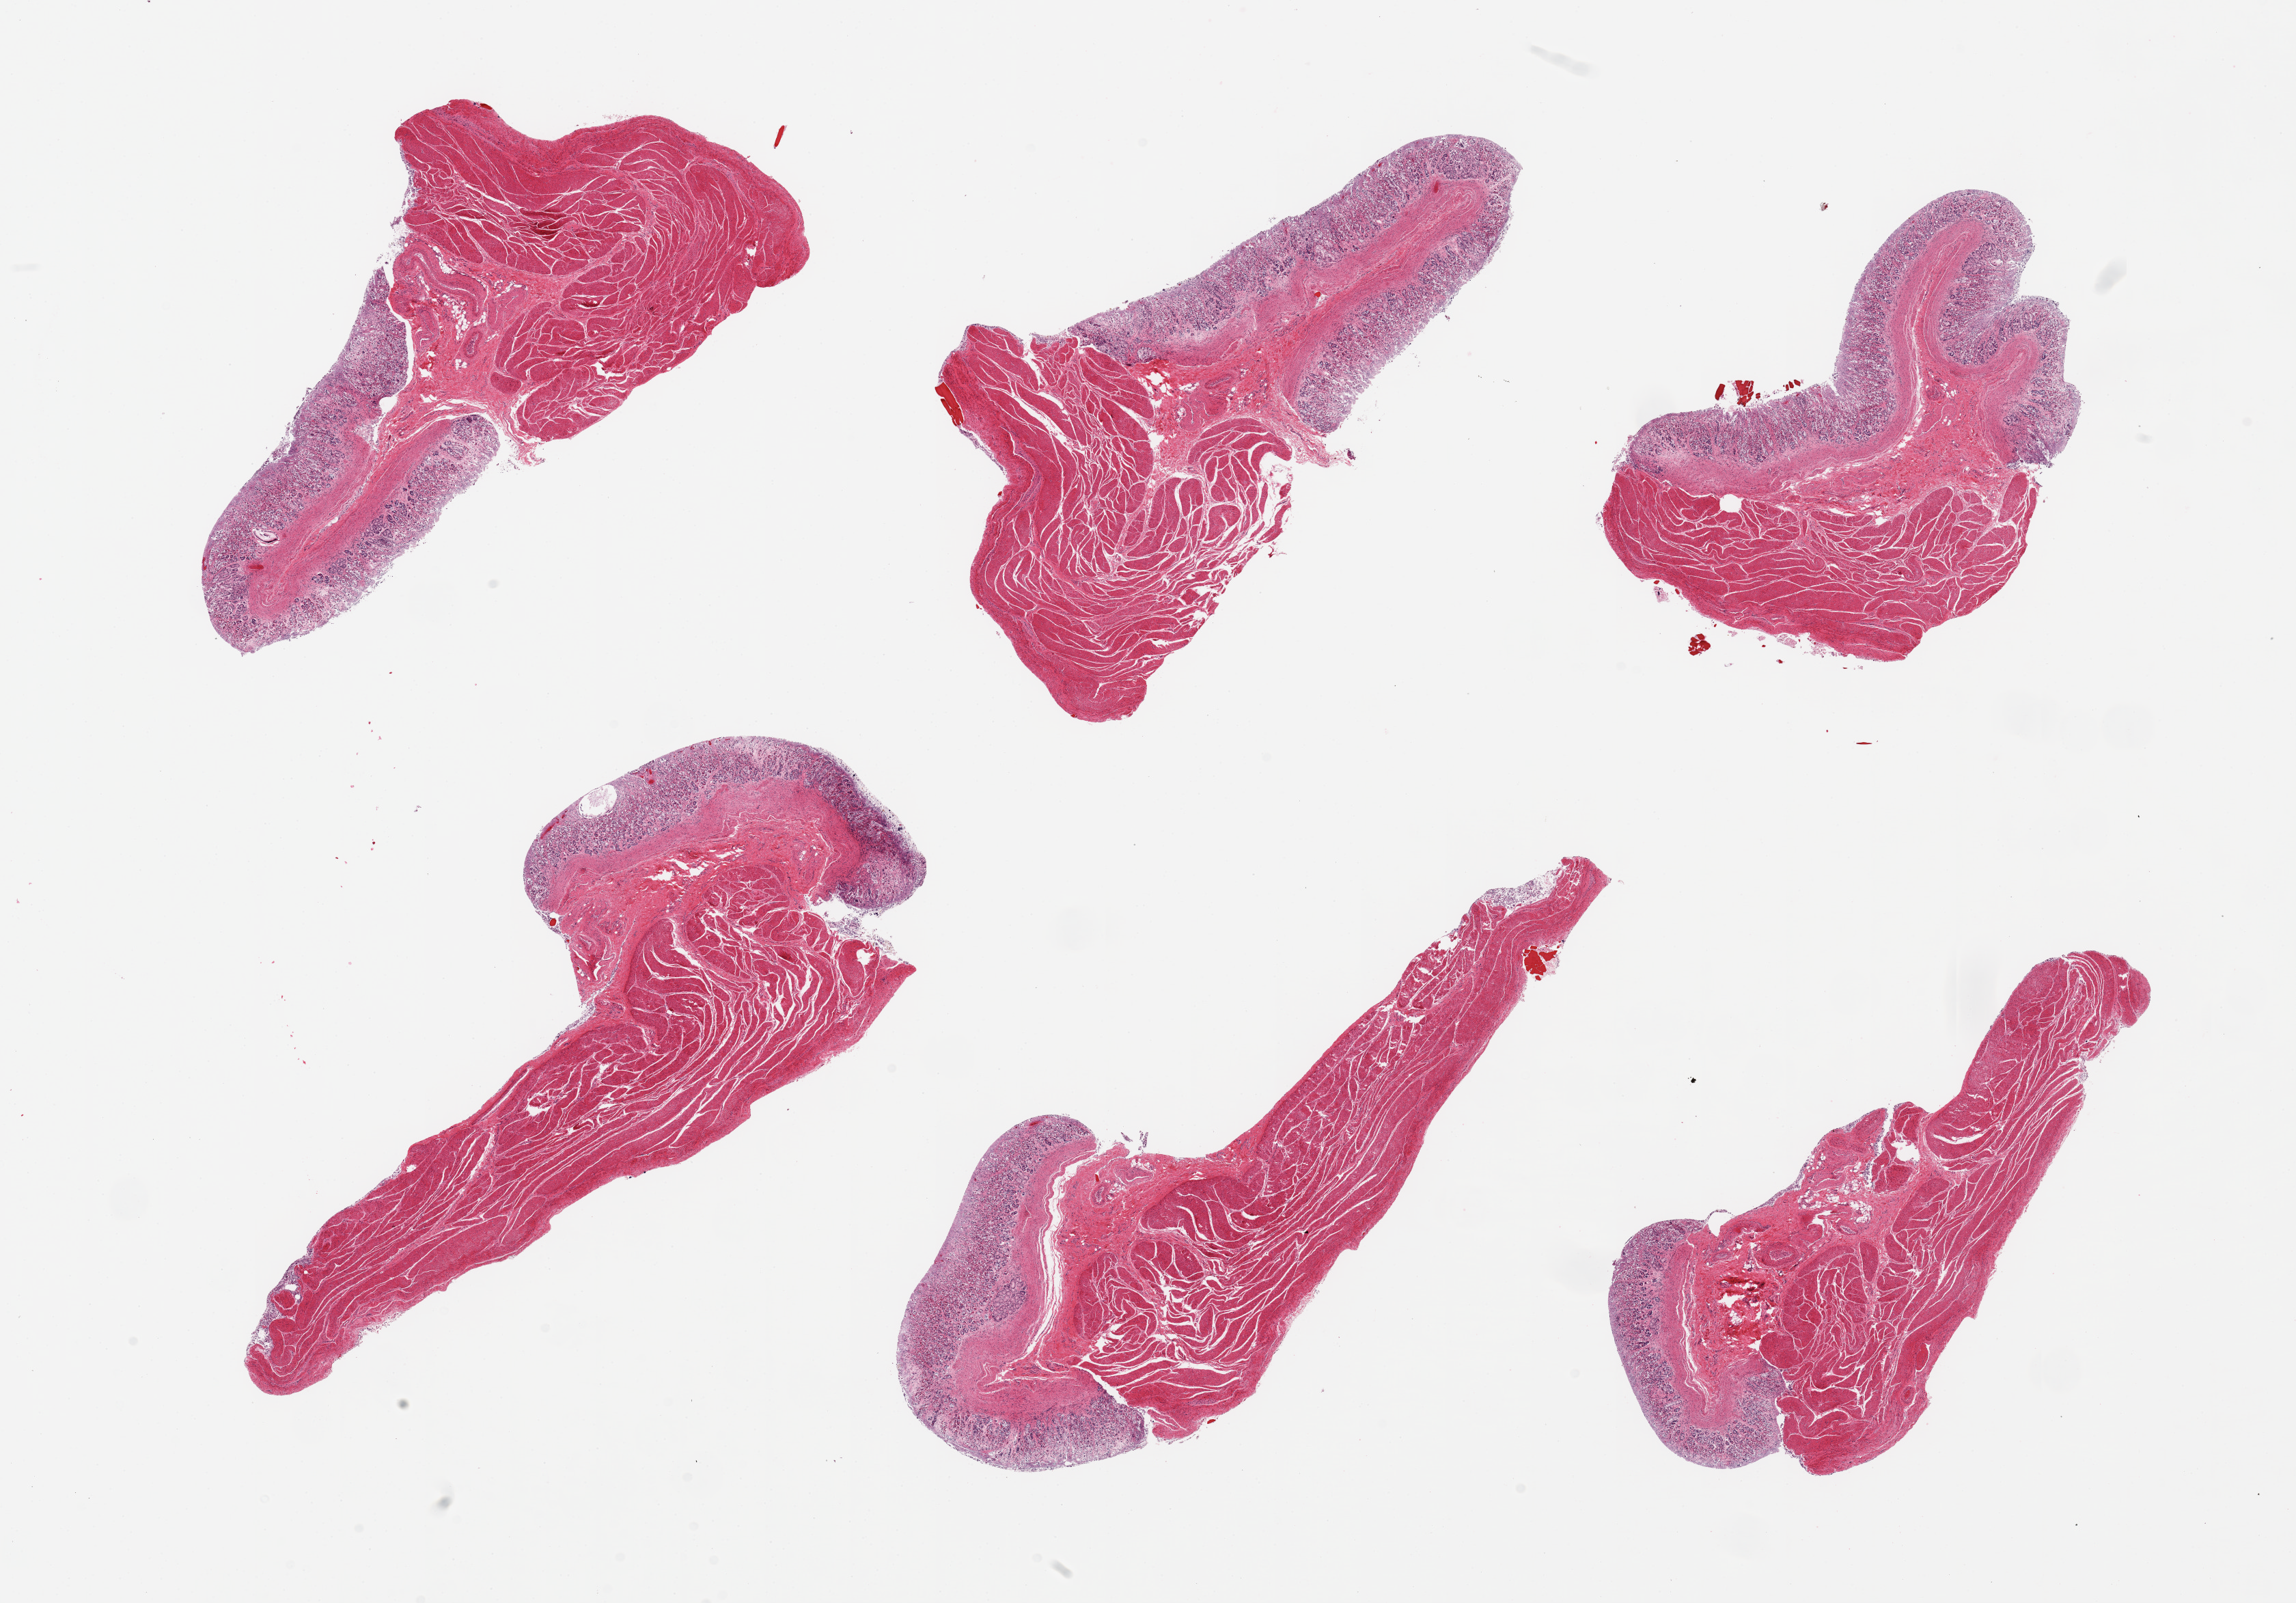
Whole-slide image, haematoxylin and eosin stain — shown as a low-resolution overview of the whole scanned area (about 26.6 x 18.6 mm). PAXgene-fixed, paraffin-embedded tissue. Sampled site (target tissue): stomach. Donor tissue sample. Donor: male.
Reviewer comment on this tissue sample: 6 pieces; muscularis and moderately autolyzed mucosa, few detached fragments of skeletal muscle.